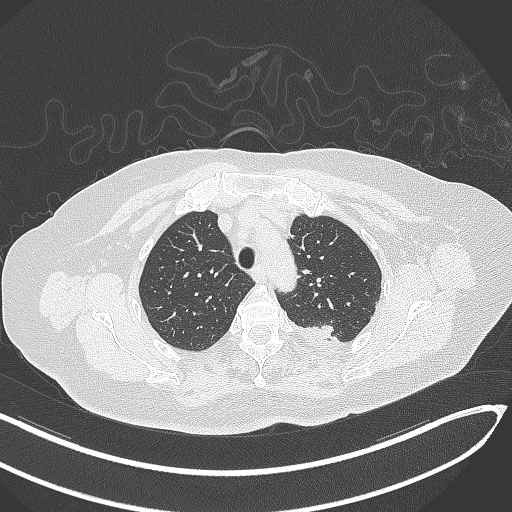
Chest CT, one axial slice. Slice 255 of 270 in the series (ordered by position). Reconstruction kernel B70f. Lung window (W 1500 / L -600 HU). 512 × 512 image matrix. Female patient, age 76 years. From the clinical record (not read from this slice): clinical TNM (as recorded): T1c N0 M0.
Outlined on this slice (rectangle marked by the reading radiologist):
- lung tumour (recorded histology: adenocarcinoma): bounding box [x1, y1, x2, y2] px = [319, 324, 336, 340]